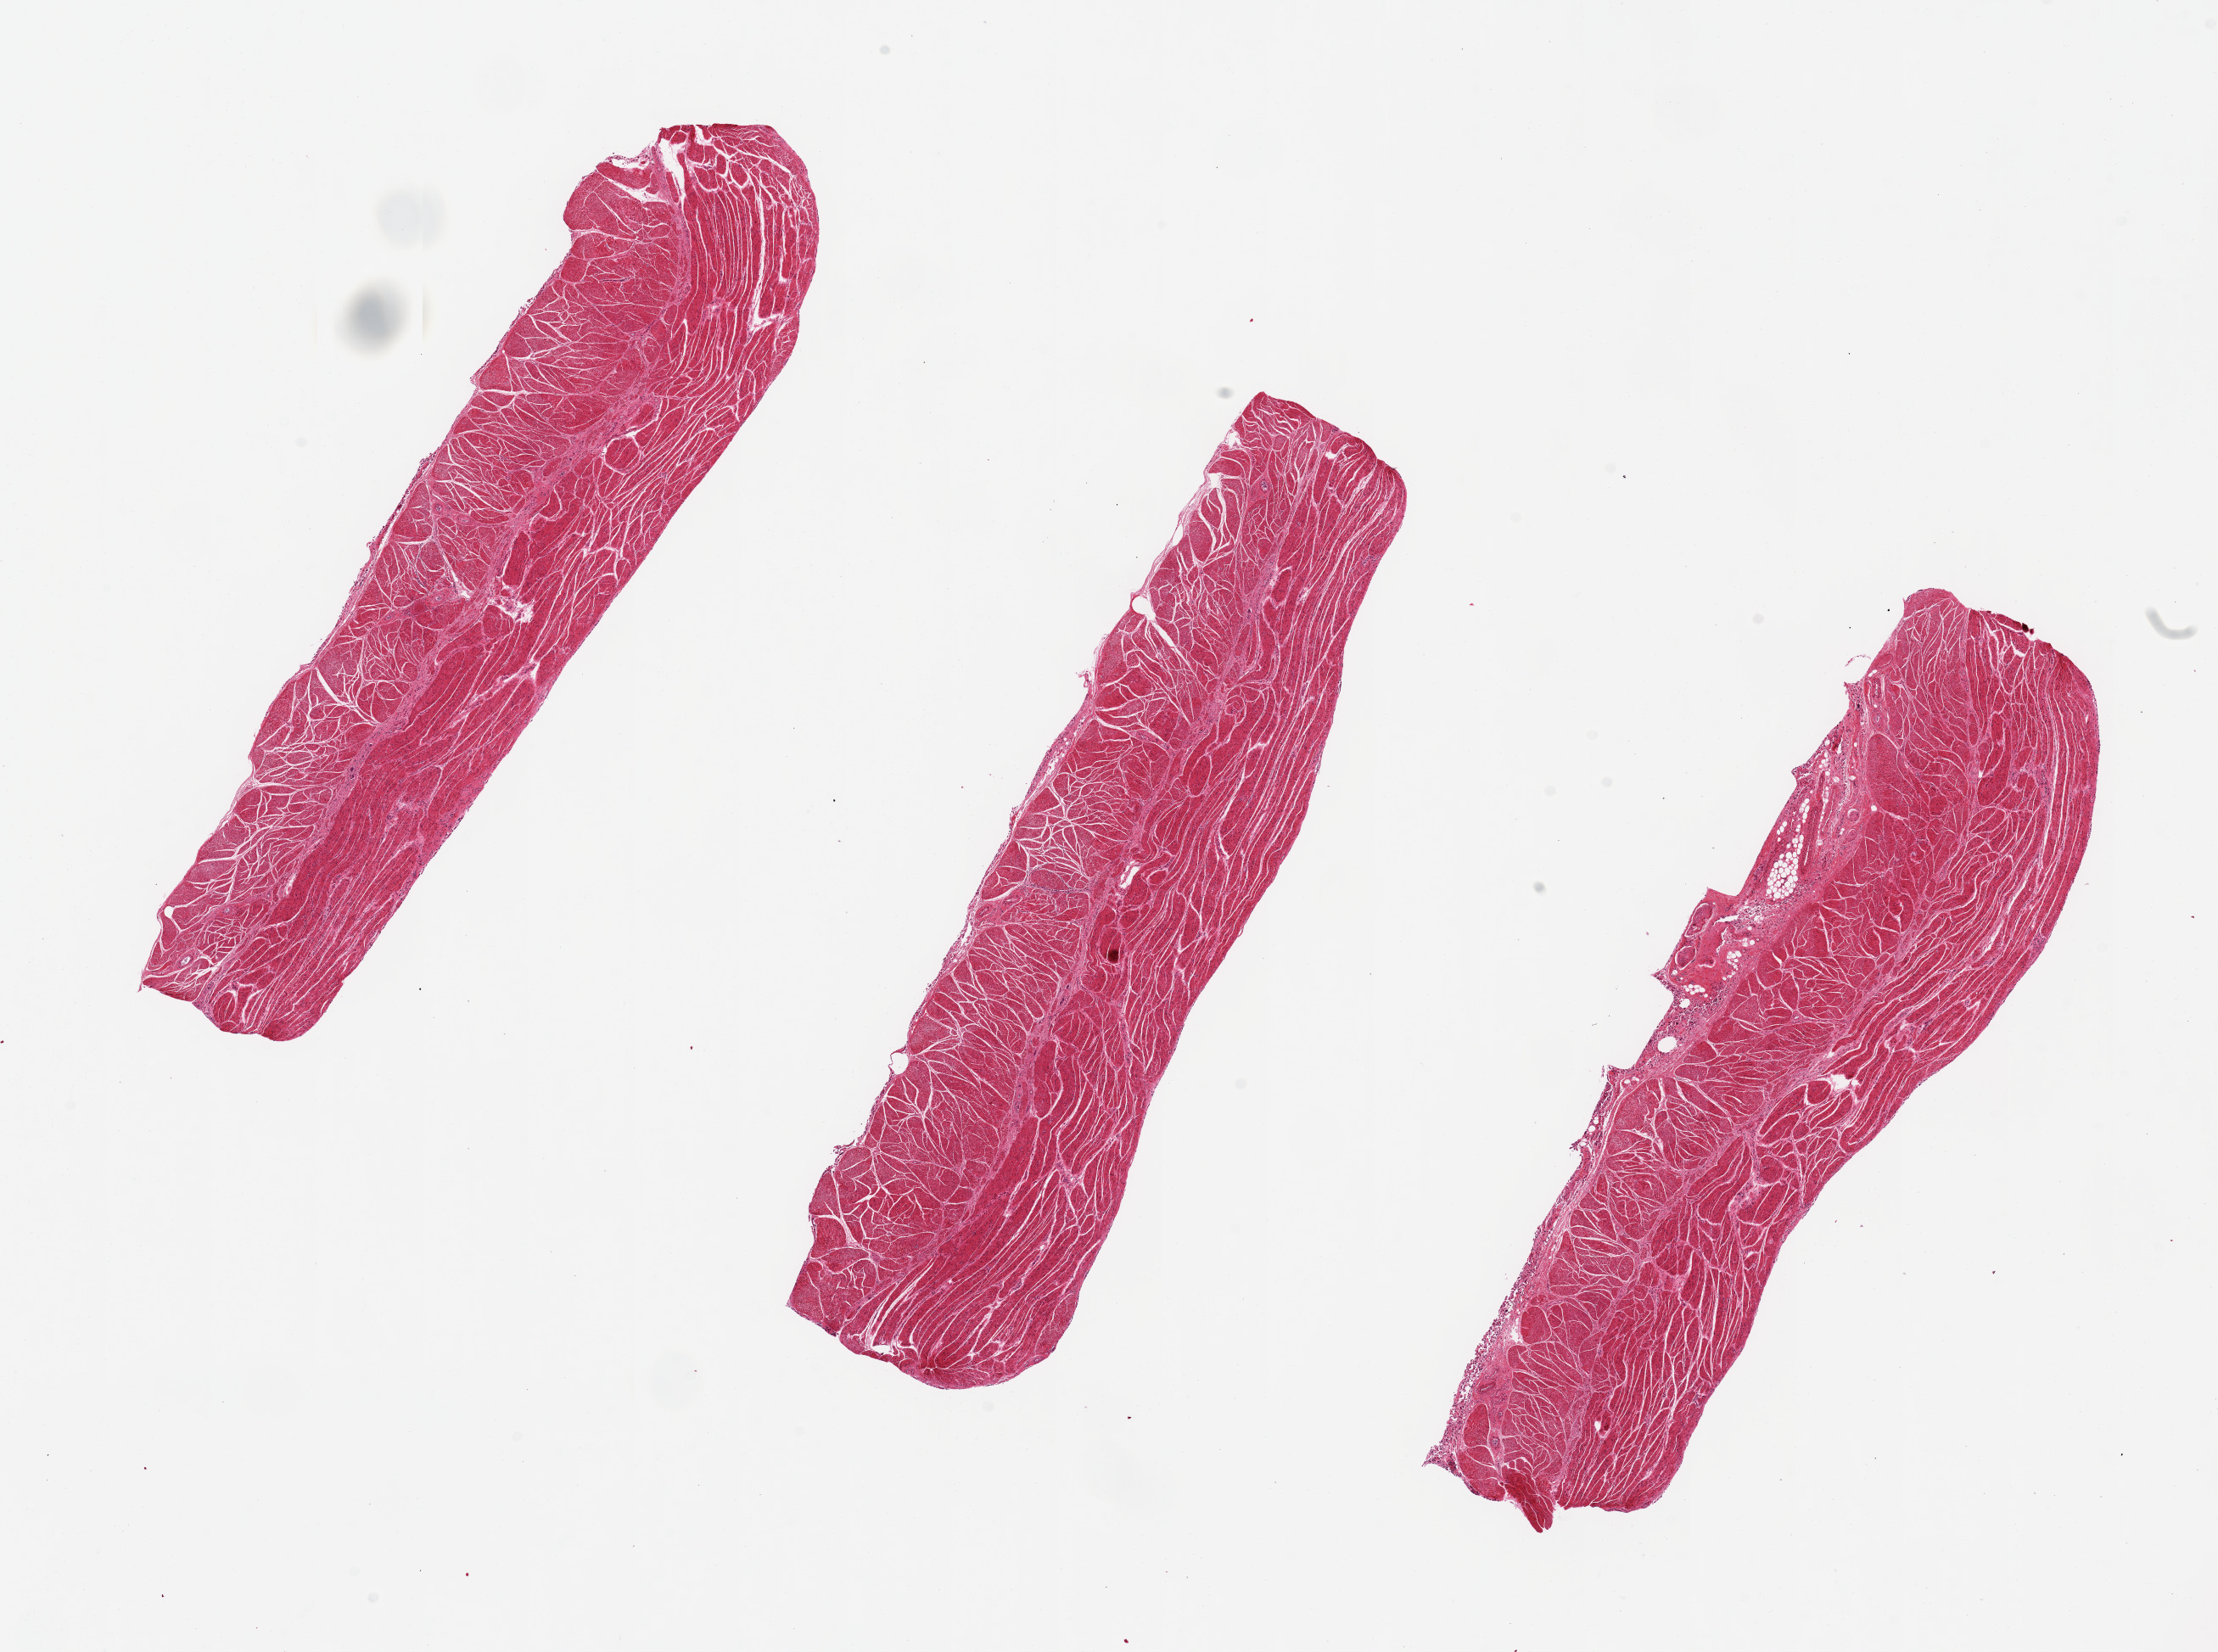
Whole-slide image, haematoxylin and eosin stain — a low-resolution overview of the entire scanned area, about 20.7 x 15.4 mm; PAXgene-fixed paraffin-embedded (PFPE) section; sampled site (target tissue): esophageal muscle; donor tissue sample. Donor sex: male.
Reviewer comment on this tissue sample: Reasonably good preservation.